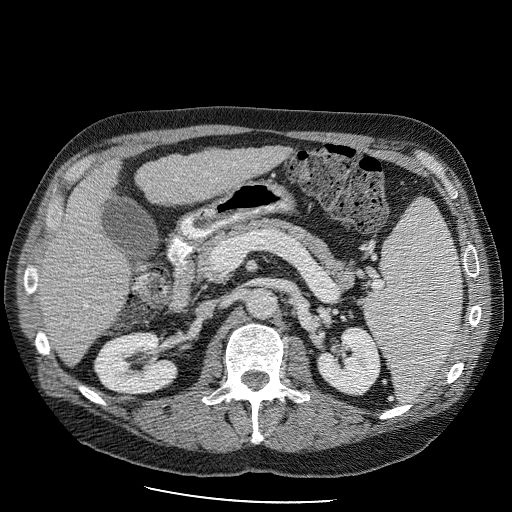
Contrast-enhanced abdominal CT (liver protocol), one axial slice; slice 41 of 98 in the series (ordered by position); reconstruction kernel STANDARD; 120 kVp; soft-tissue window (W 400 / L 40 HU); 512 × 512 image matrix, field of view 400 × 400 mm. Case-level facts recorded for this patient, not image findings: diagnosis: hepatocellular carcinoma (patient treated with transarterial chemoembolisation; whether this scan precedes or follows treatment is not stated here); TNM stage (as recorded): Stage-II; Child-Pugh class: B.
Outlined on this slice (semi-automatically segmented with operator editing):
- liver parenchyma outside the tumour (the mass and vessels are separate outlines, so this box may not span the whole liver): box from (x=38, y=144) to (x=294, y=364) px